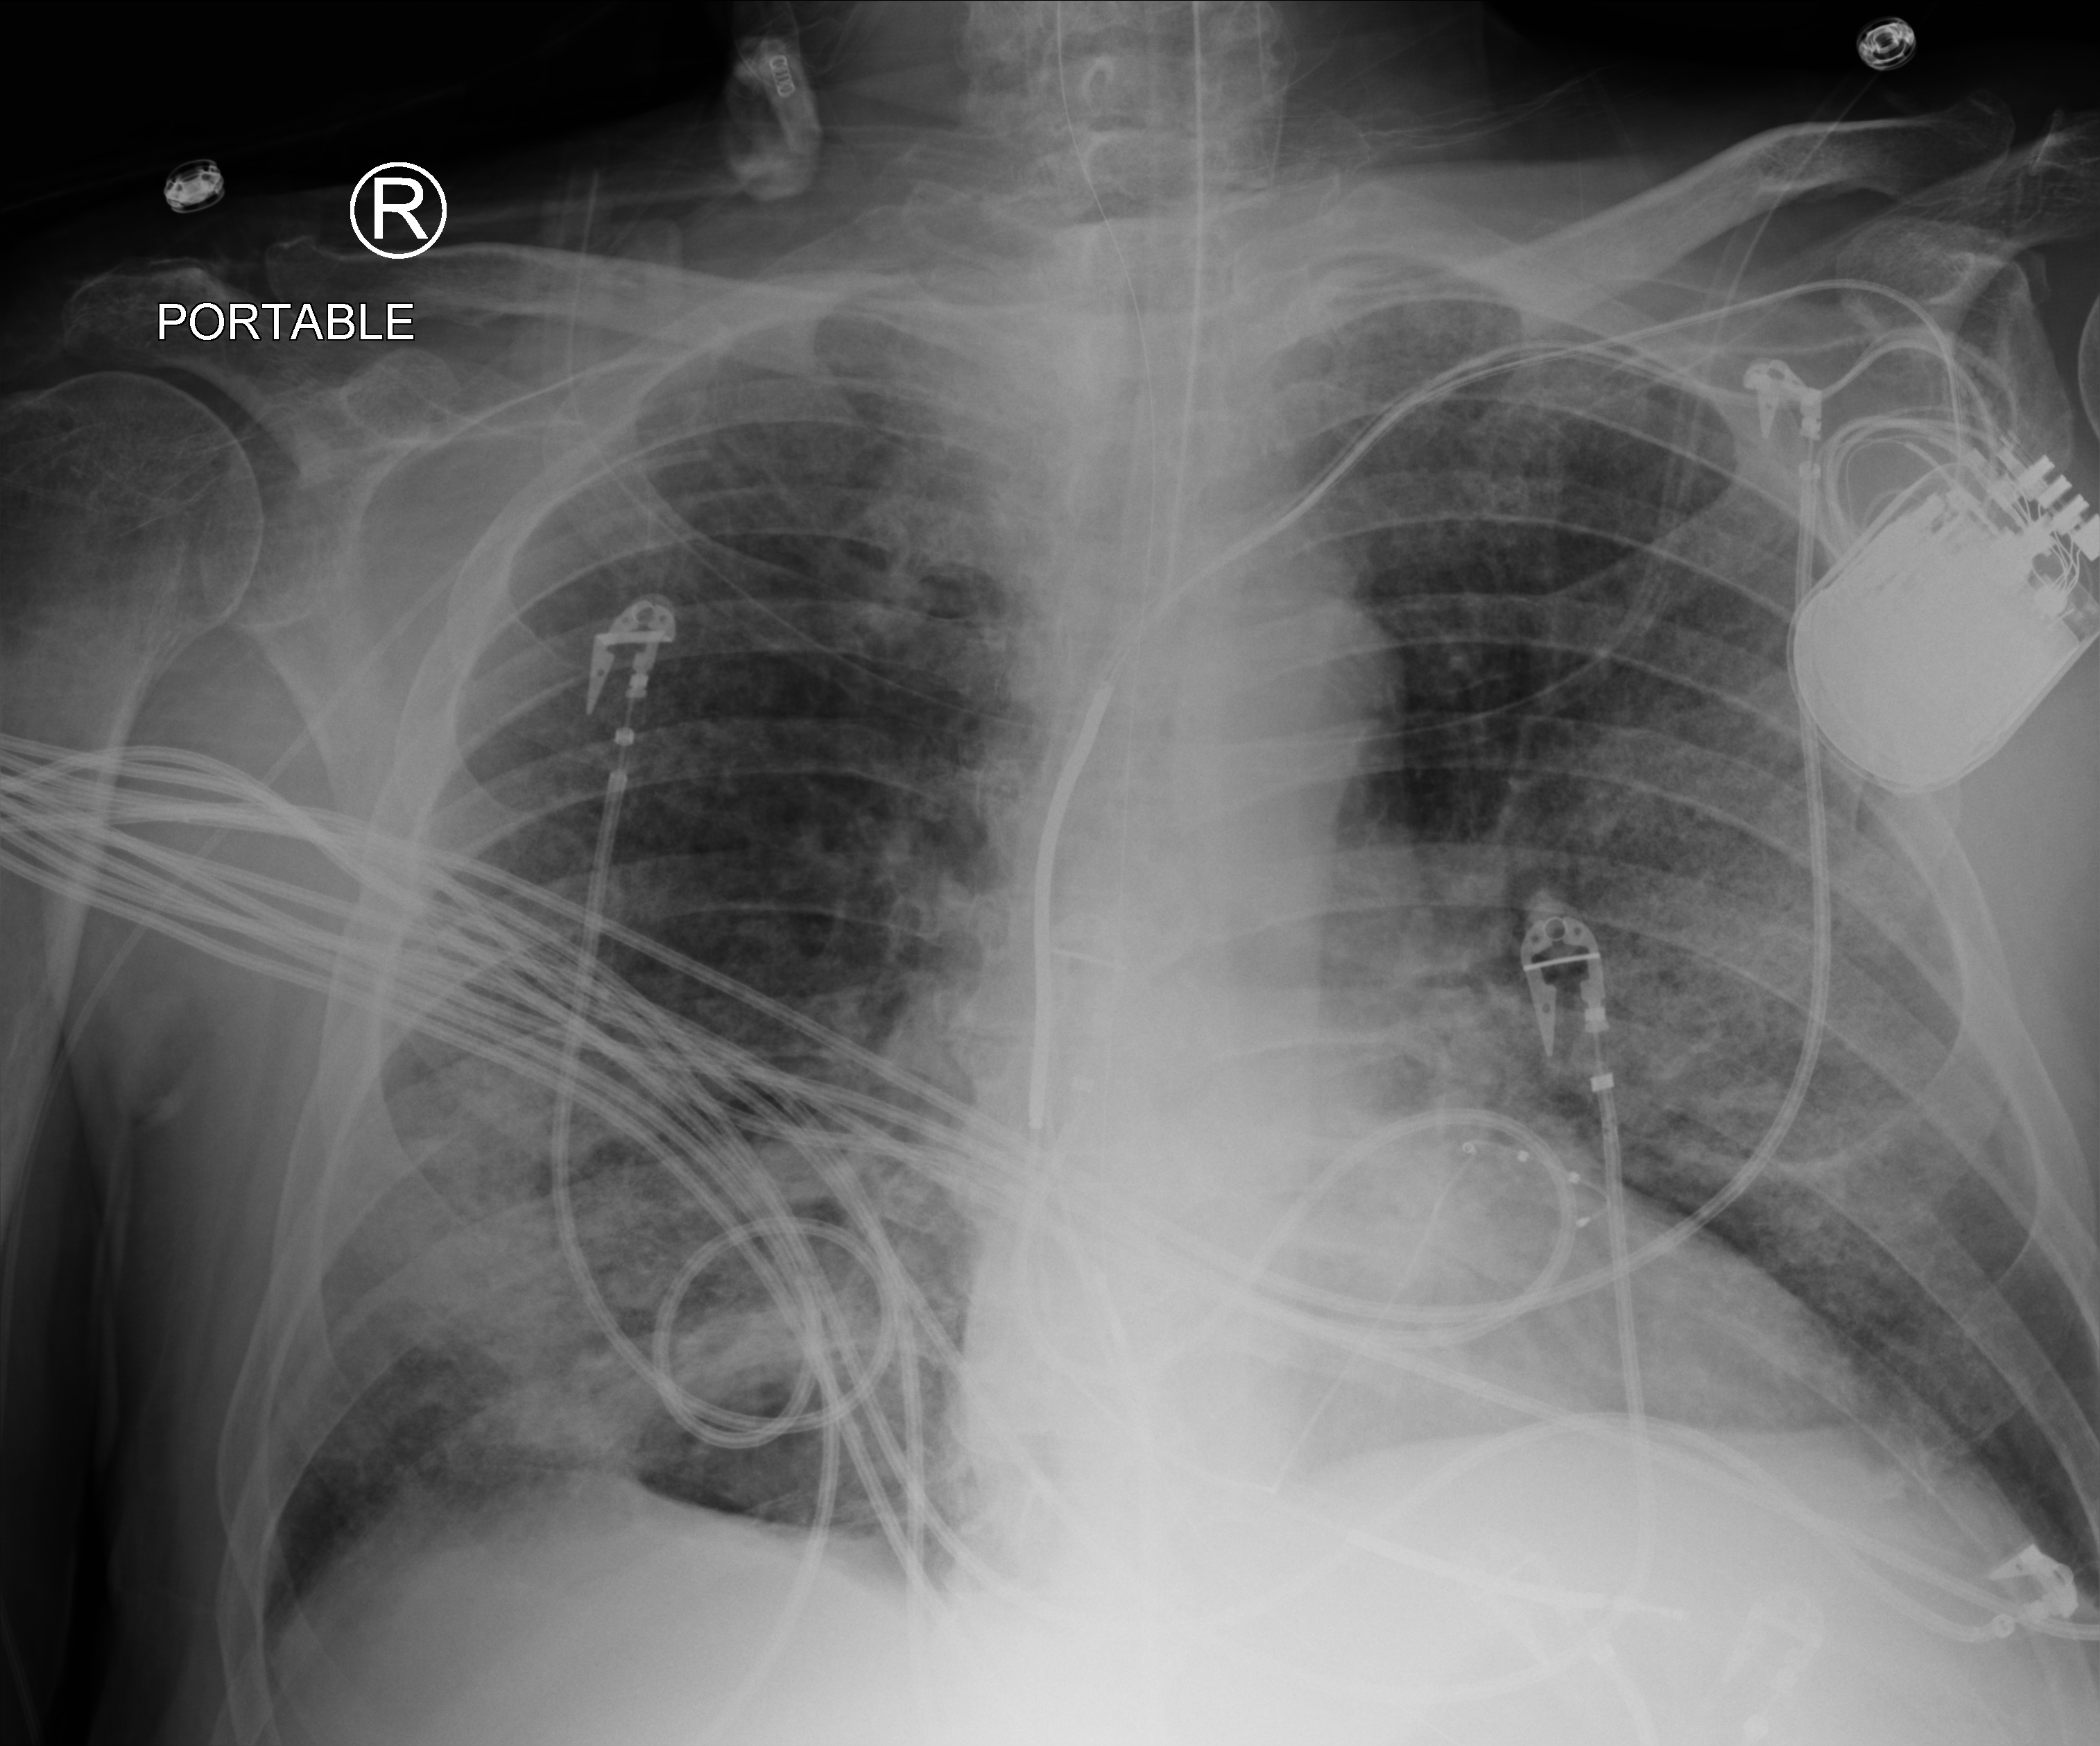
Chest X-ray (portable), anteroposterior (AP) projection. Male patient hospitalised with COVID-19, age 60–74 years.
Hospital-stay facts (about this admission, not read from this image; timing relative to this image not recorded):
- length of hospital stay: 36 days
- mechanically ventilated during this hospital stay: yes
- admitted to intensive care during this hospital stay: yes